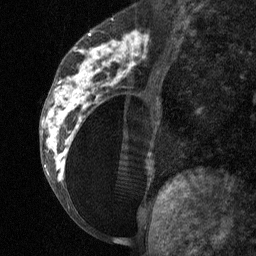
Breast MRI (dynamic contrast-enhanced), one sagittal slice; slice 30 of 64 in the series (ordered by position); dynamic contrast-enhanced study with each time point stored as its own series, time point 2 of 3 at this slice position (early post-contrast, ordered by acquisition time); 1.5 T; TE 4.8 ms, TR 27 ms; 256 × 256 image matrix, field of view 180 × 180 mm. Female patient, age 34 years. From the clinical record (not read from this slice): setting: breast cancer imaged before/during neoadjuvant chemotherapy; receptor status: HR-positive, HER2-negative.
Outlined on this slice (semi-automatically segmented with operator editing):
- analysis volume of interest (the breast-tissue region the enhancement analysis was run in; not a lesion): bounding box <41,23,157,197> (left, top, right, bottom; pixels)
- tumour enhancement mask (voxels above the 90 % enhancement threshold inside the analysis volume of interest): <42,31,143,181>